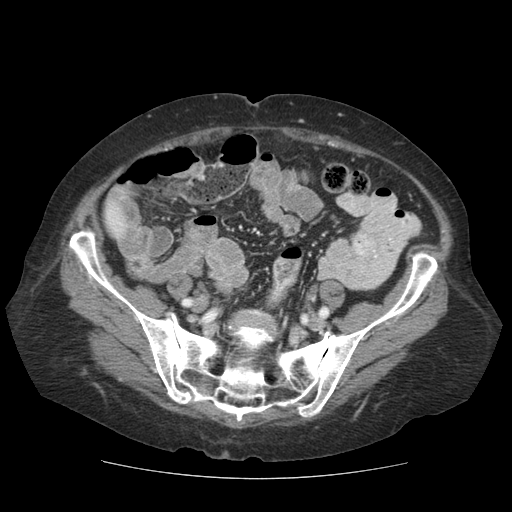
Contrast-enhanced abdominal CT (liver protocol), one axial slice; soft-tissue window (W 400 / L 40 HU); 512 × 512 image matrix. From the clinical record (not read from this slice): diagnosis: hepatocellular carcinoma (patient treated with transarterial chemoembolisation; whether this scan precedes or follows treatment is not stated here); TNM stage (as recorded): Stage-I; Child-Pugh class: A; tumour differentiation: moderately-poorly differentiated; tumour size: 7.3 cm.
Structures marked on this image (semi-automatically segmented with operator editing):
- liver parenchyma outside the tumour (the mass and vessels are separate outlines, so this box may not span the whole liver): box from (x=104, y=193) to (x=148, y=262) px